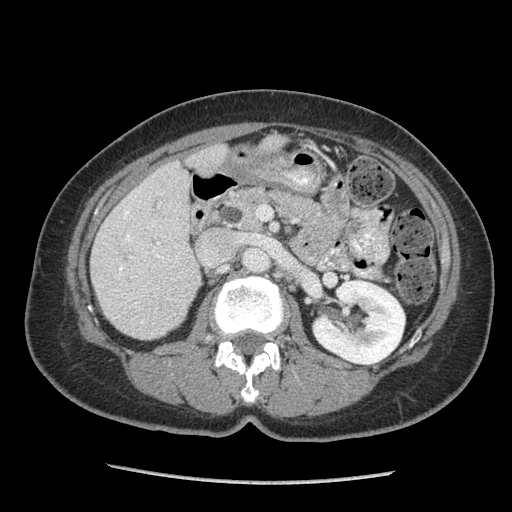
Contrast-enhanced abdominal CT (liver protocol), one axial slice. Slice 34 of 105 in the series (ordered by position). Soft-tissue window (W 400 / L 40 HU). 2.5 mm slice thickness. 512 × 512 image matrix, field of view 340 × 340 mm. From the clinical record (not read from this slice): diagnosis: hepatocellular carcinoma (patient treated with transarterial chemoembolisation; whether this scan precedes or follows treatment is not stated here); TNM stage (as recorded): Stage-I; Child-Pugh class: A; tumour nodularity: uninodular; tumour size: 11.1 cm.
Structures marked on this image (semi-automatic segmentation, software-assisted and operator-edited):
- liver parenchyma outside the tumour (the mass and vessels are separate outlines, so this box may not span the whole liver): bounding box (x1, y1, x2, y2) in pixels: (90, 138, 274, 338)
- liver vessels: (118, 203, 177, 323)